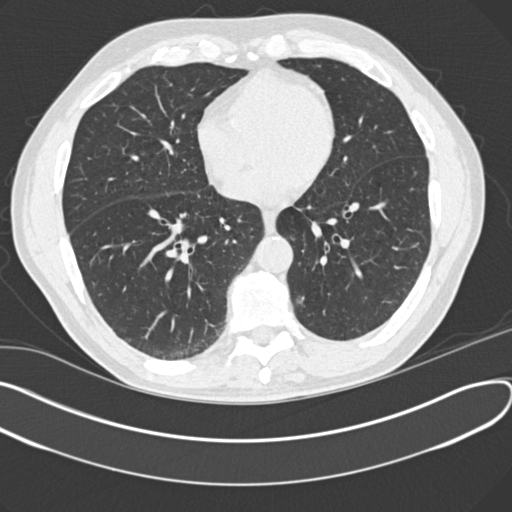
Low-dose screening chest CT, one axial slice; lung window (W 1500 / L -600 HU); 2 mm slice thickness; 512 × 512 image matrix.
Structures marked on this image (manually delineated by an expert):
- lesion 1 (tumor, lower lobe of left lung): bounding box (x1, y1, x2, y2) in pixels: (295, 294, 306, 306)